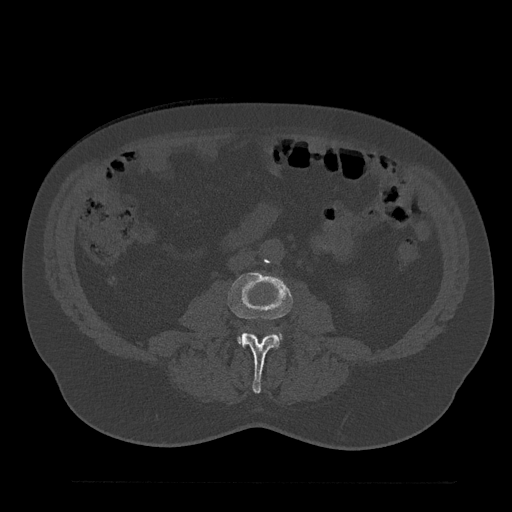
CT including the spine, one axial slice. Slice 14 of 797 in the series (ordered by position). Reconstruction kernel Br40s/3. Bone window (W 1800 / L 400 HU). 0.5 mm slice thickness. 512 × 512 image matrix, field of view 430 × 430 mm. Patient: male, 61 years. Case-level facts recorded for this patient, not image findings: primary cancer: prostate.
Outlined on this slice (semi-automatic segmentation, software-assisted and operator-edited):
- L3 vertebra: bounding box [x1, y1, x2, y2] px = [228, 272, 292, 394]
- L4 vertebra: [239, 337, 243, 344]